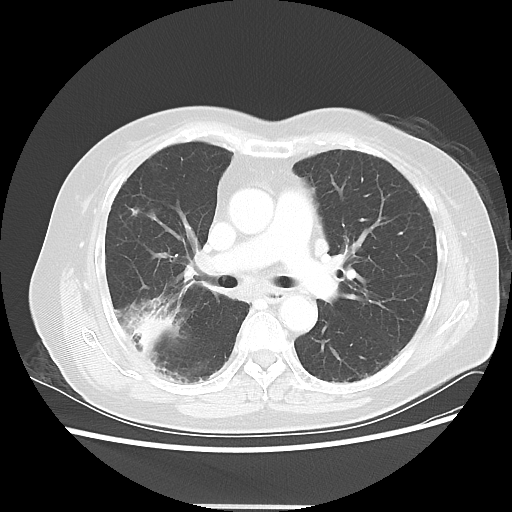
Chest CT, one axial slice. Slice 28 of 50 in the series (ordered by position). 120 kVp. Lung window (W 1500 / L -600 HU). 5 mm slice thickness. 512 × 512 image matrix. Female patient, age 72 years. Case-level facts recorded for this patient, not image findings: clinical TNM (as recorded): T2 N1 M0; histopathological grade: G1.
Structures marked on this image (bounding box drawn by a radiologist):
- lung tumour (recorded histology: adenocarcinoma): bounding box [x1, y1, x2, y2] px = [130, 315, 173, 351]